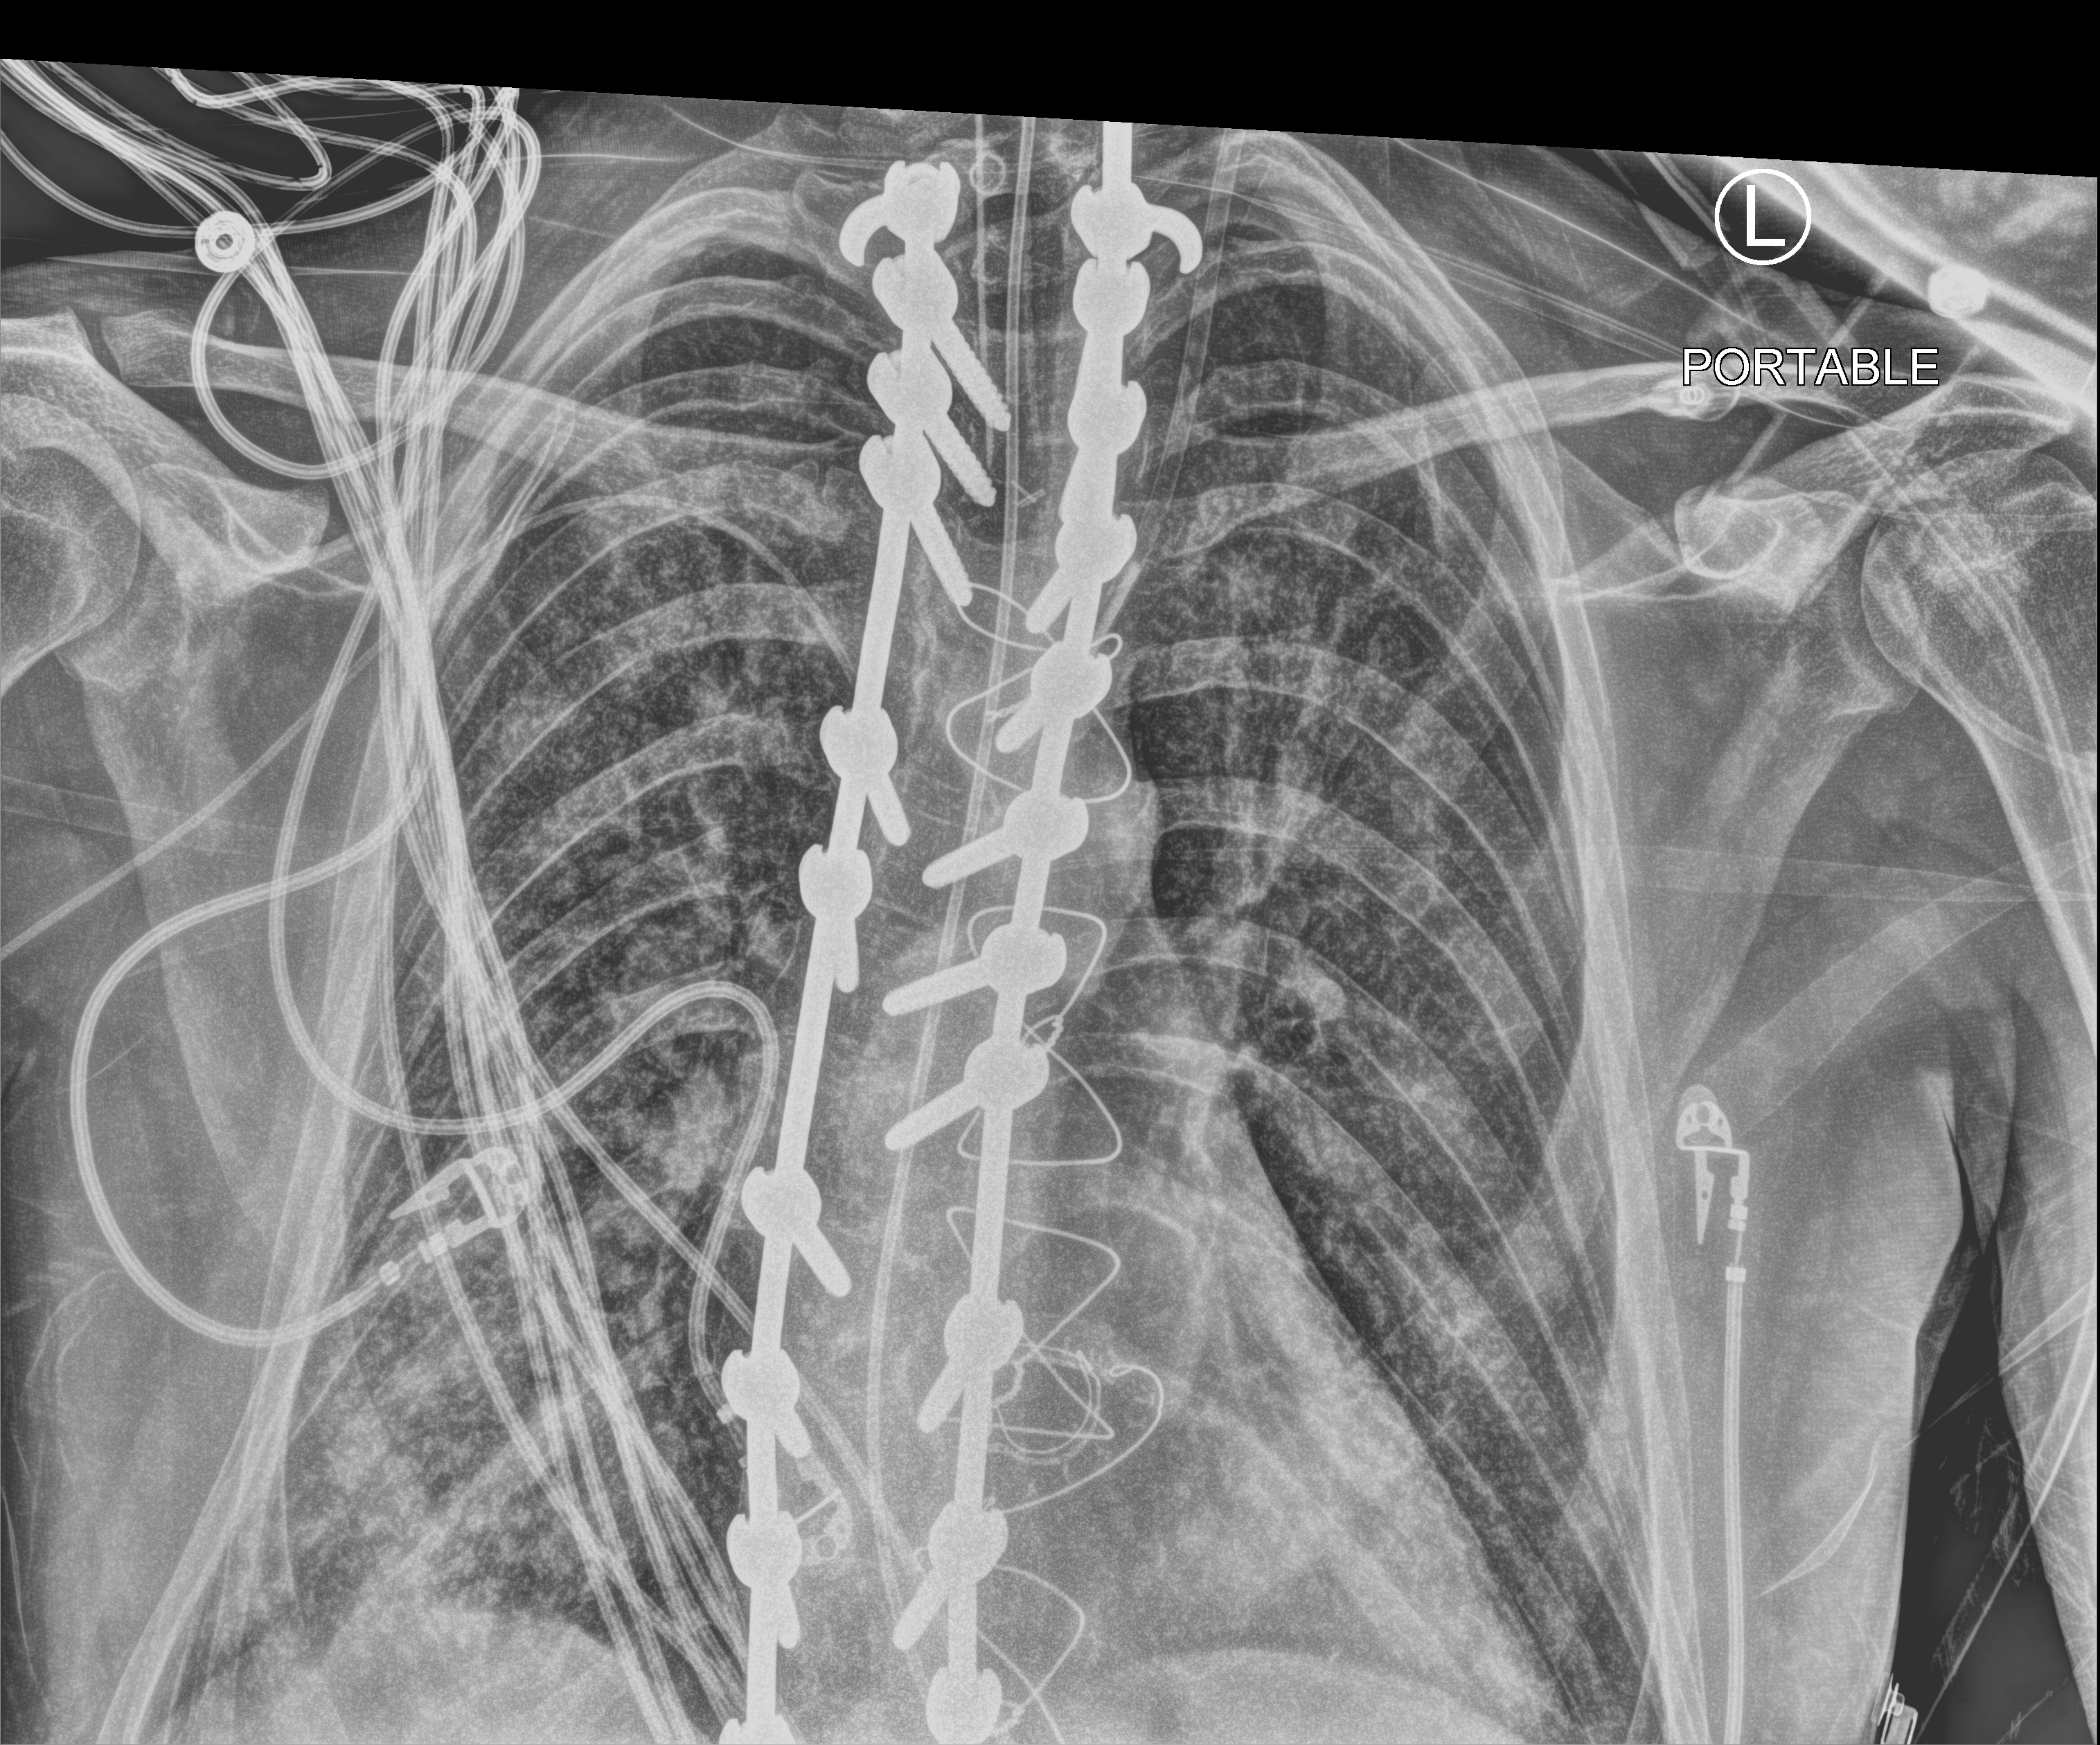
Portable chest radiograph, anteroposterior (AP) projection. Patient hospitalised with COVID-19, aged 18–59 years.
From the hospital-stay record, not from the radiograph (when in the stay this image was taken is not recorded):
- length of hospital stay: 15 days
- admitted to intensive care during this hospital stay: yes